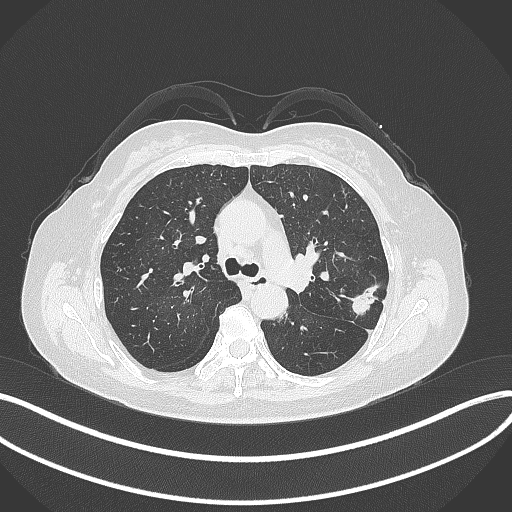
Chest CT, one axial slice. Slice 210 of 319 in the series (ordered by position). Reconstruction kernel B70f. 120 kVp. Lung window (W 1500 / L -600 HU). 1 mm slice thickness. 512 × 512 image matrix. Female patient, age 60 years. From the clinical record (not read from this slice): clinical TNM (as recorded): T1c N0 M0.
Structures marked on this image (rectangle marked by the reading radiologist):
- lung tumour (recorded histology: adenocarcinoma): bounding box [x1, y1, x2, y2] px = [349, 279, 383, 321]